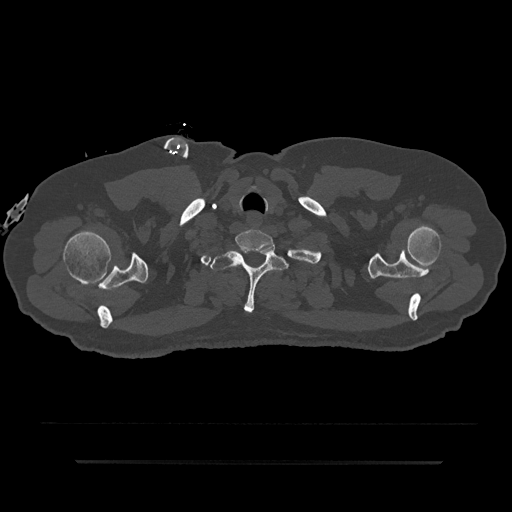
CT including the spine, one axial slice; position 747 of 797 along the scan axis; reconstruction kernel Br40s/3; 120 kVp; bone window (W 1800 / L 400 HU); 0.5 mm slice thickness; 512 × 512 image matrix. Male patient, age 59 years. From the clinical record (not read from this slice): primary cancer: bile ducts; vertebrae with lytic lesions (as recorded): T10.
Annotated regions visible in this slice (semi-automatic segmentation, software-assisted and operator-edited):
- T1 vertebra: bounding box (x1, y1, x2, y2) in pixels: (210, 247, 288, 313)